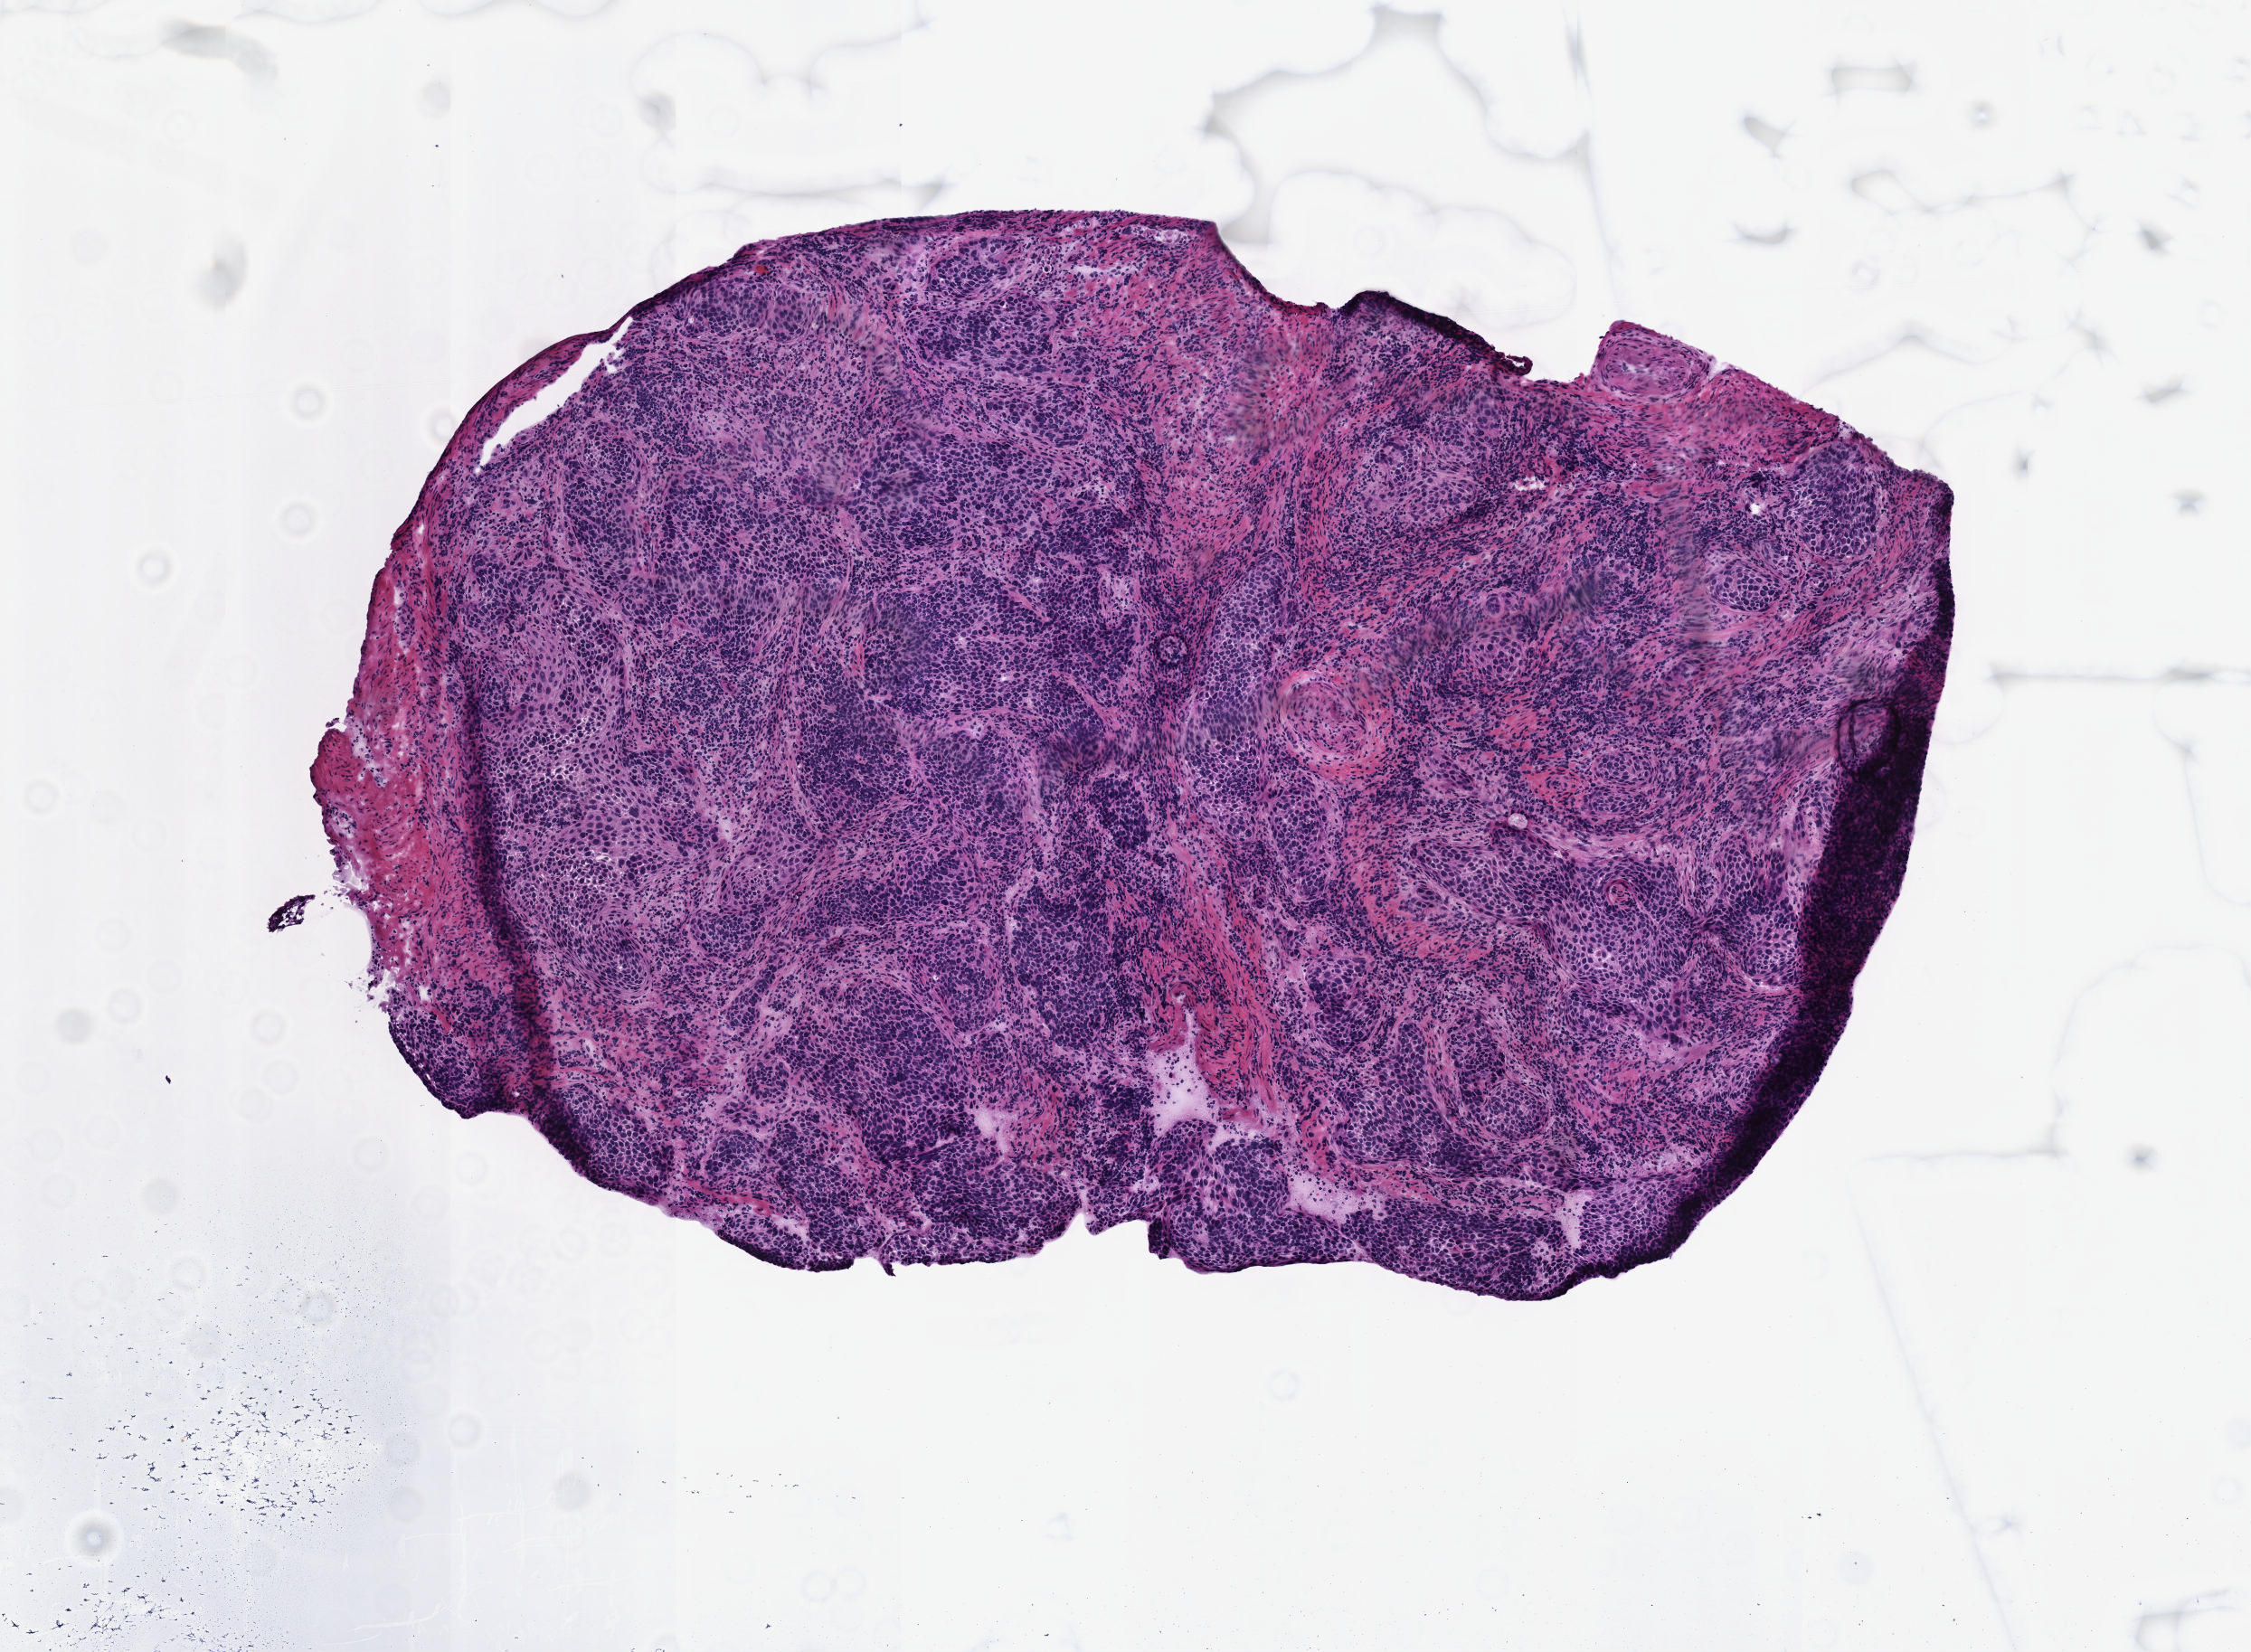
H&E whole-slide image, shown as a low-resolution overview of the whole scanned area (about 5.0 x 3.7 mm), frozen section, cervix, primary tumour sample. Female, age 41 years at initial diagnosis. Histologic grade: G2 (moderately differentiated). Composition of this section per pathologist review: tumour cells 70%, tumour nuclei 70%, normal cells 10%, stromal cells 20%, necrosis 0%. Inflammatory infiltration, as recorded: lymphocyte infiltration 15%, monocyte infiltration 0%, neutrophil infiltration 0%.
- FIGO stage: IB1
- diagnosis: Squamous cell carcinoma, large cell, nonkeratinizing, NOS (cervix uteri)